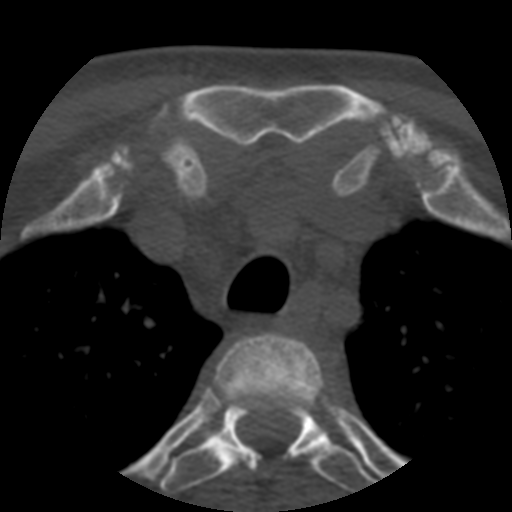
CT including the spine, one axial slice; slice 421 of 508 in the series (ordered by position); 120 kVp; bone window (W 1800 / L 400 HU); 1.25 mm slice thickness; 512 × 512 image matrix, field of view 160 × 160 mm. Patient age 57 years. From the clinical record (not read from this slice): primary cancer: prostate.
Outlined on this slice (semi-automatic segmentation, software-assisted and operator-edited):
- T2 vertebra: bounding box (x1, y1, x2, y2) in pixels: (210, 333, 327, 406)
- T3 vertebra: (161, 399, 376, 493)